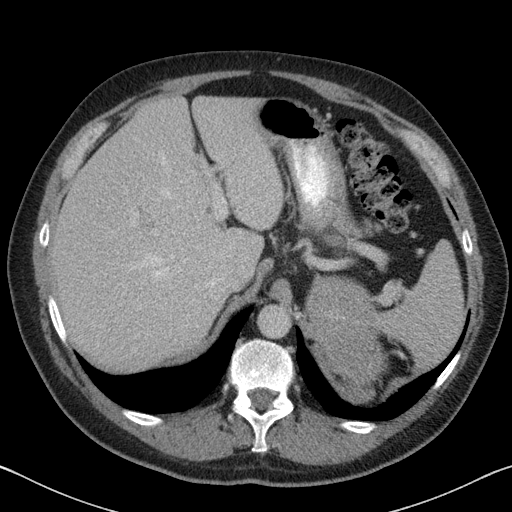
Contrast-enhanced abdominal CT, one axial slice; slice 62 of 88 in the series (ordered by position); reconstruction kernel B31f; 120 kVp; intravenous contrast given; soft-tissue window (W 400 / L 40 HU); 3 mm slice thickness; 512 × 512 image matrix, field of view 366 × 366 mm. Patient: male, 51 years. Case-level facts recorded for this patient, not image findings: diagnosis: adrenocortical carcinoma; tumour side: left adrenal; tumour size at pathology: 16.5 cm; Ki-67 index: 30 %; stage (as recorded): 2.
Structures marked on this image (semi-automatically segmented with operator editing):
- mass: bounding box [x1, y1, x2, y2] px = [312, 278, 380, 385]